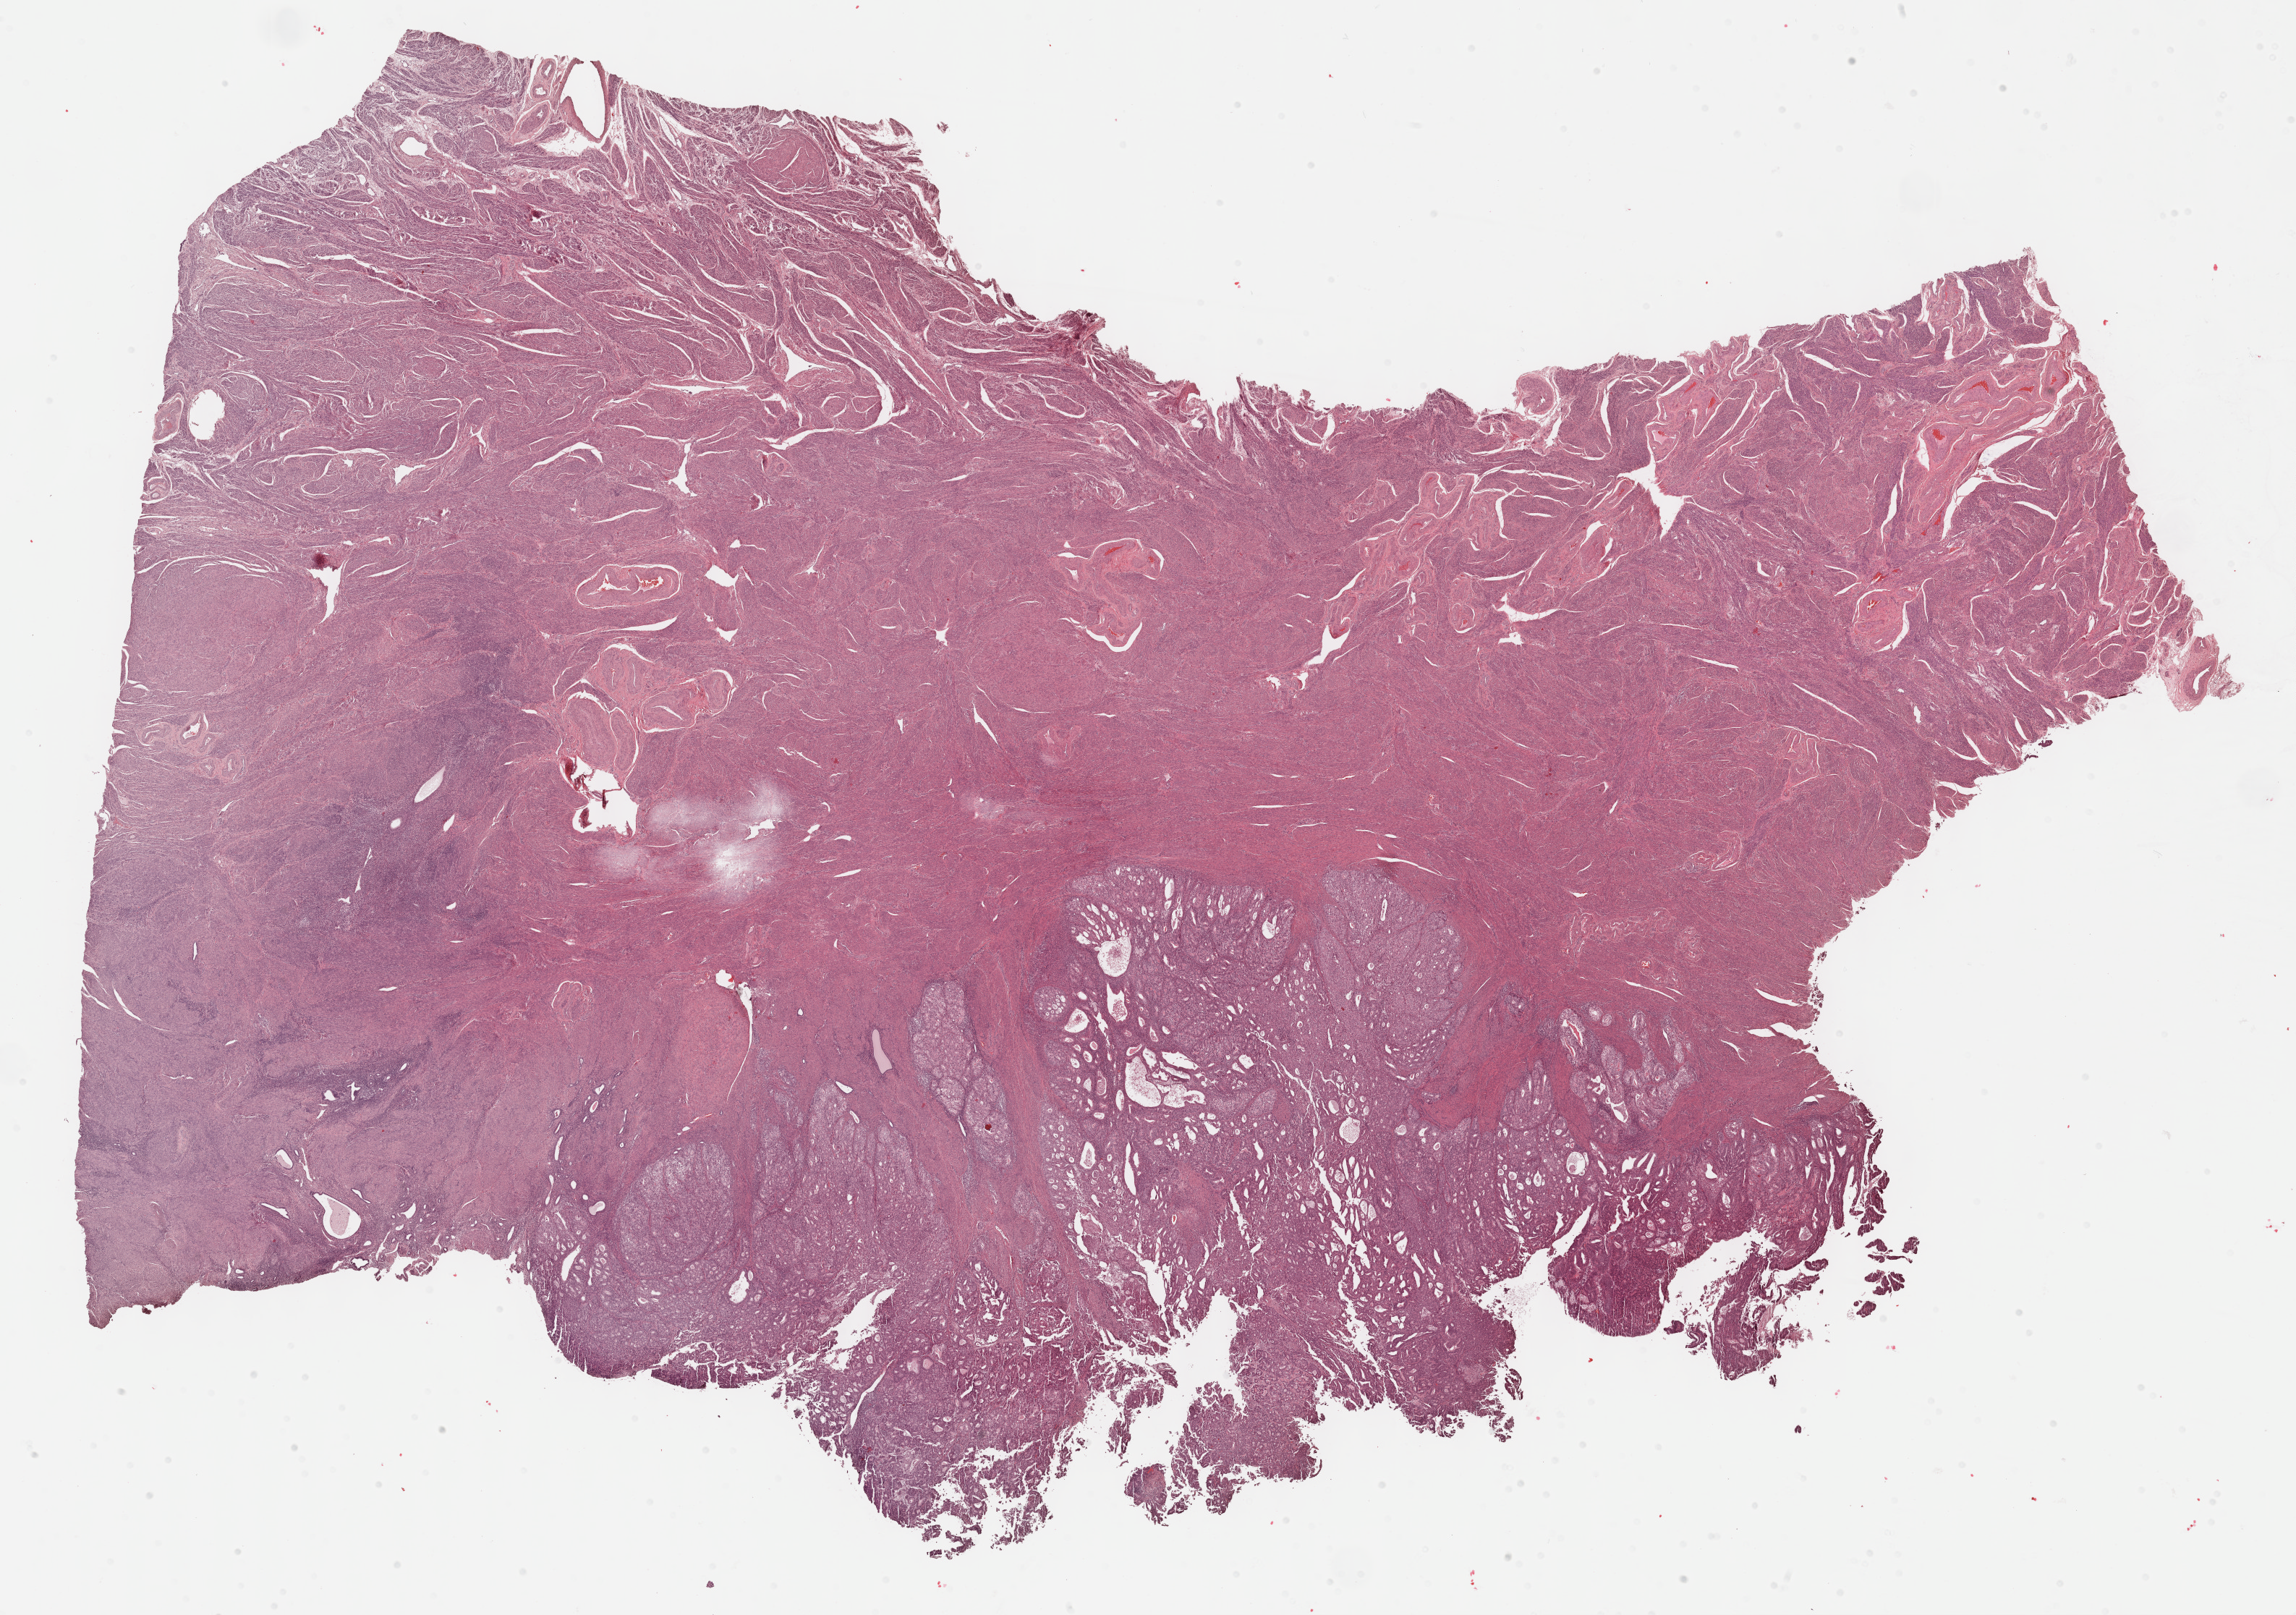
Whole-slide histology image, H&E-stained, whole scanned area (about 25.7 x 18.1 mm, slide scanned at 40x) shown as a low-resolution overview. Formalin-fixed paraffin-embedded (FFPE) diagnostic section. Primary tumour sample from the uterus. Female patient; age at initial diagnosis 64 years. Histologic grade: G1 (well differentiated).
* lymph nodes positive (case pathology): 0 of 5 examined
* pathologic diagnosis: Endometrioid adenocarcinoma, NOS (endometrium)
* FIGO stage: IB